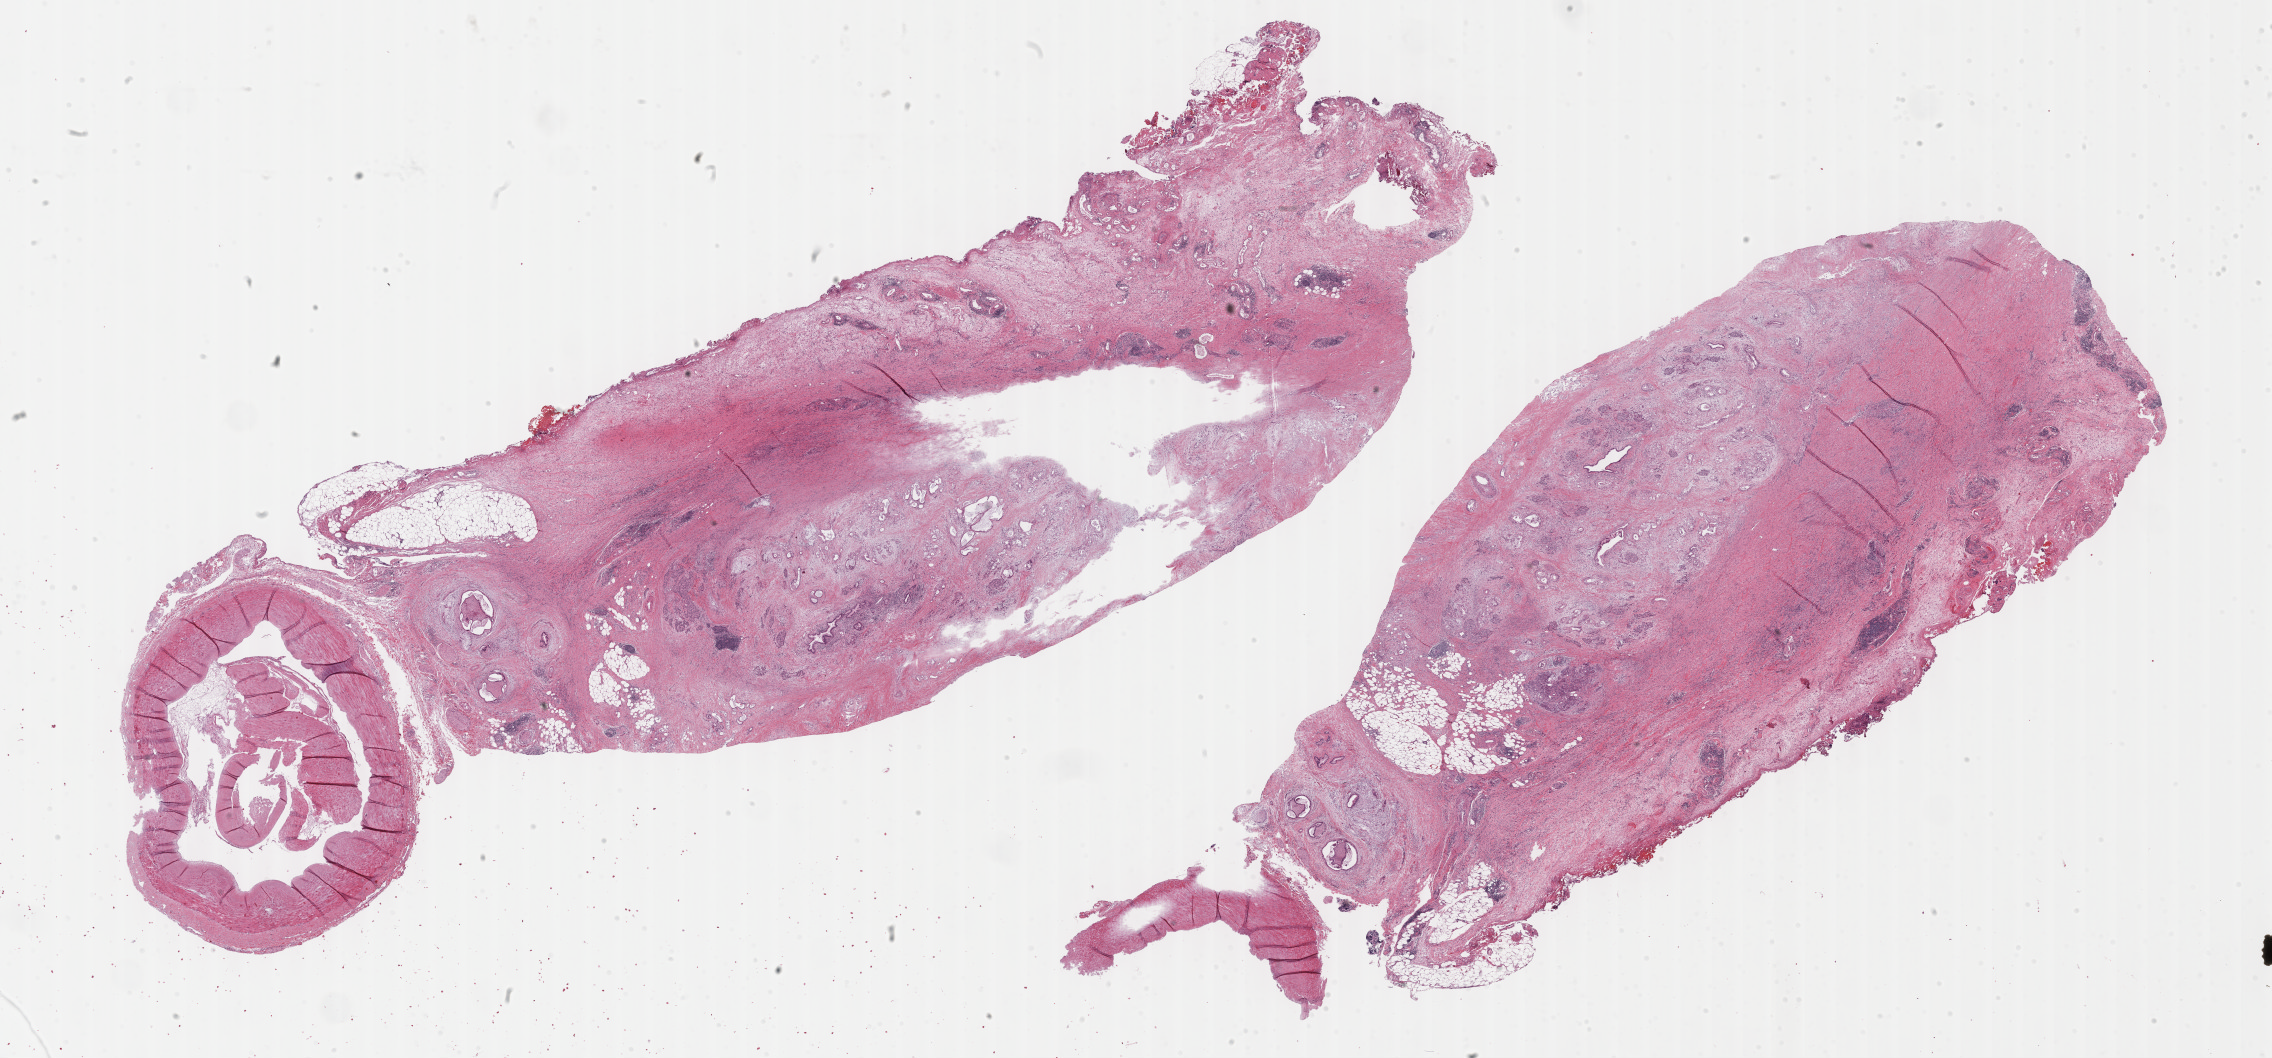
H&E-stained whole-slide image, a low-resolution overview of the entire scanned area, about 36.7 x 17.1 mm (acquisition: 40x scan). Formalin-fixed paraffin-embedded (FFPE) diagnostic section. Sample: primary tumour, pancreas. Male, age 61 years at initial diagnosis. Histologic grade: G3 (poorly differentiated).
Histologic diagnosis: Adenocarcinoma, NOS. AJCC pathologic stage: IIA (7th edition).